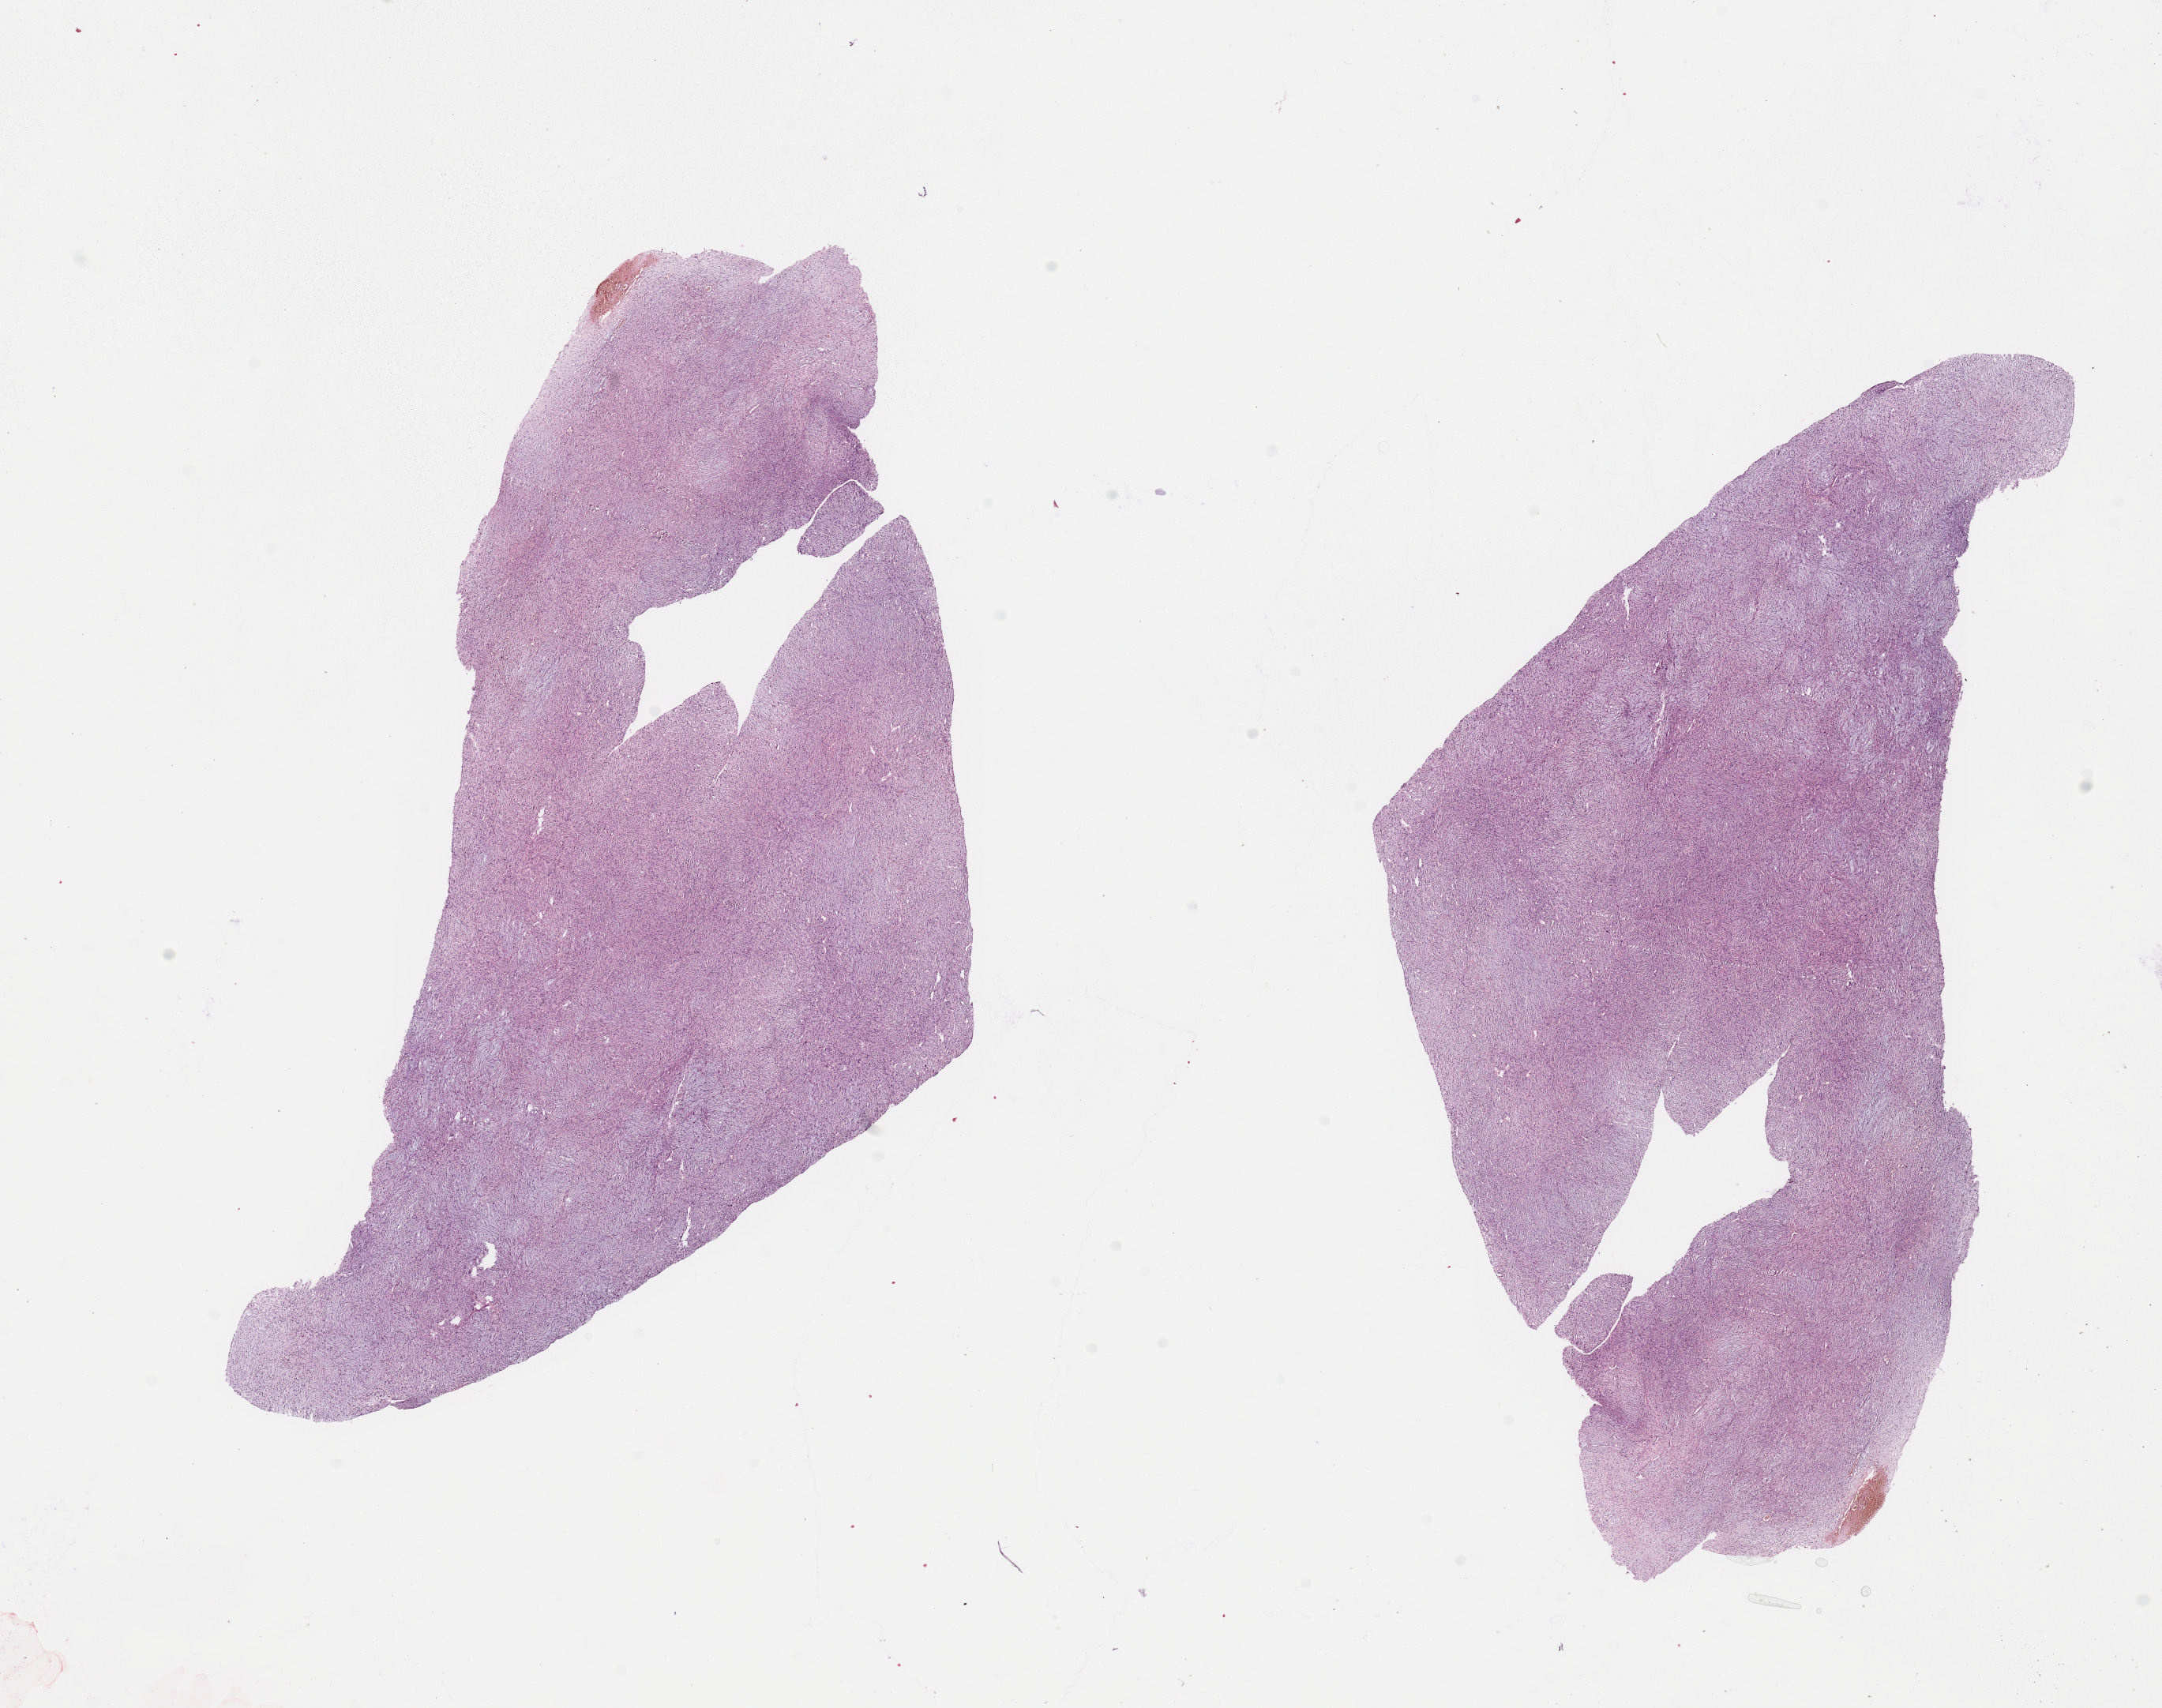
Whole-slide histology image, H&E-stained — shown as a low-resolution overview of the whole scanned area (about 21.7 x 17.1 mm, from a 20x scan). Tumour tissue sample. 72-year-old female patient.
Primary tumour site (as recorded): superficial trunk. Patient diagnosis (cohort enrolment): sarcoma (site not recorded at cohort level).